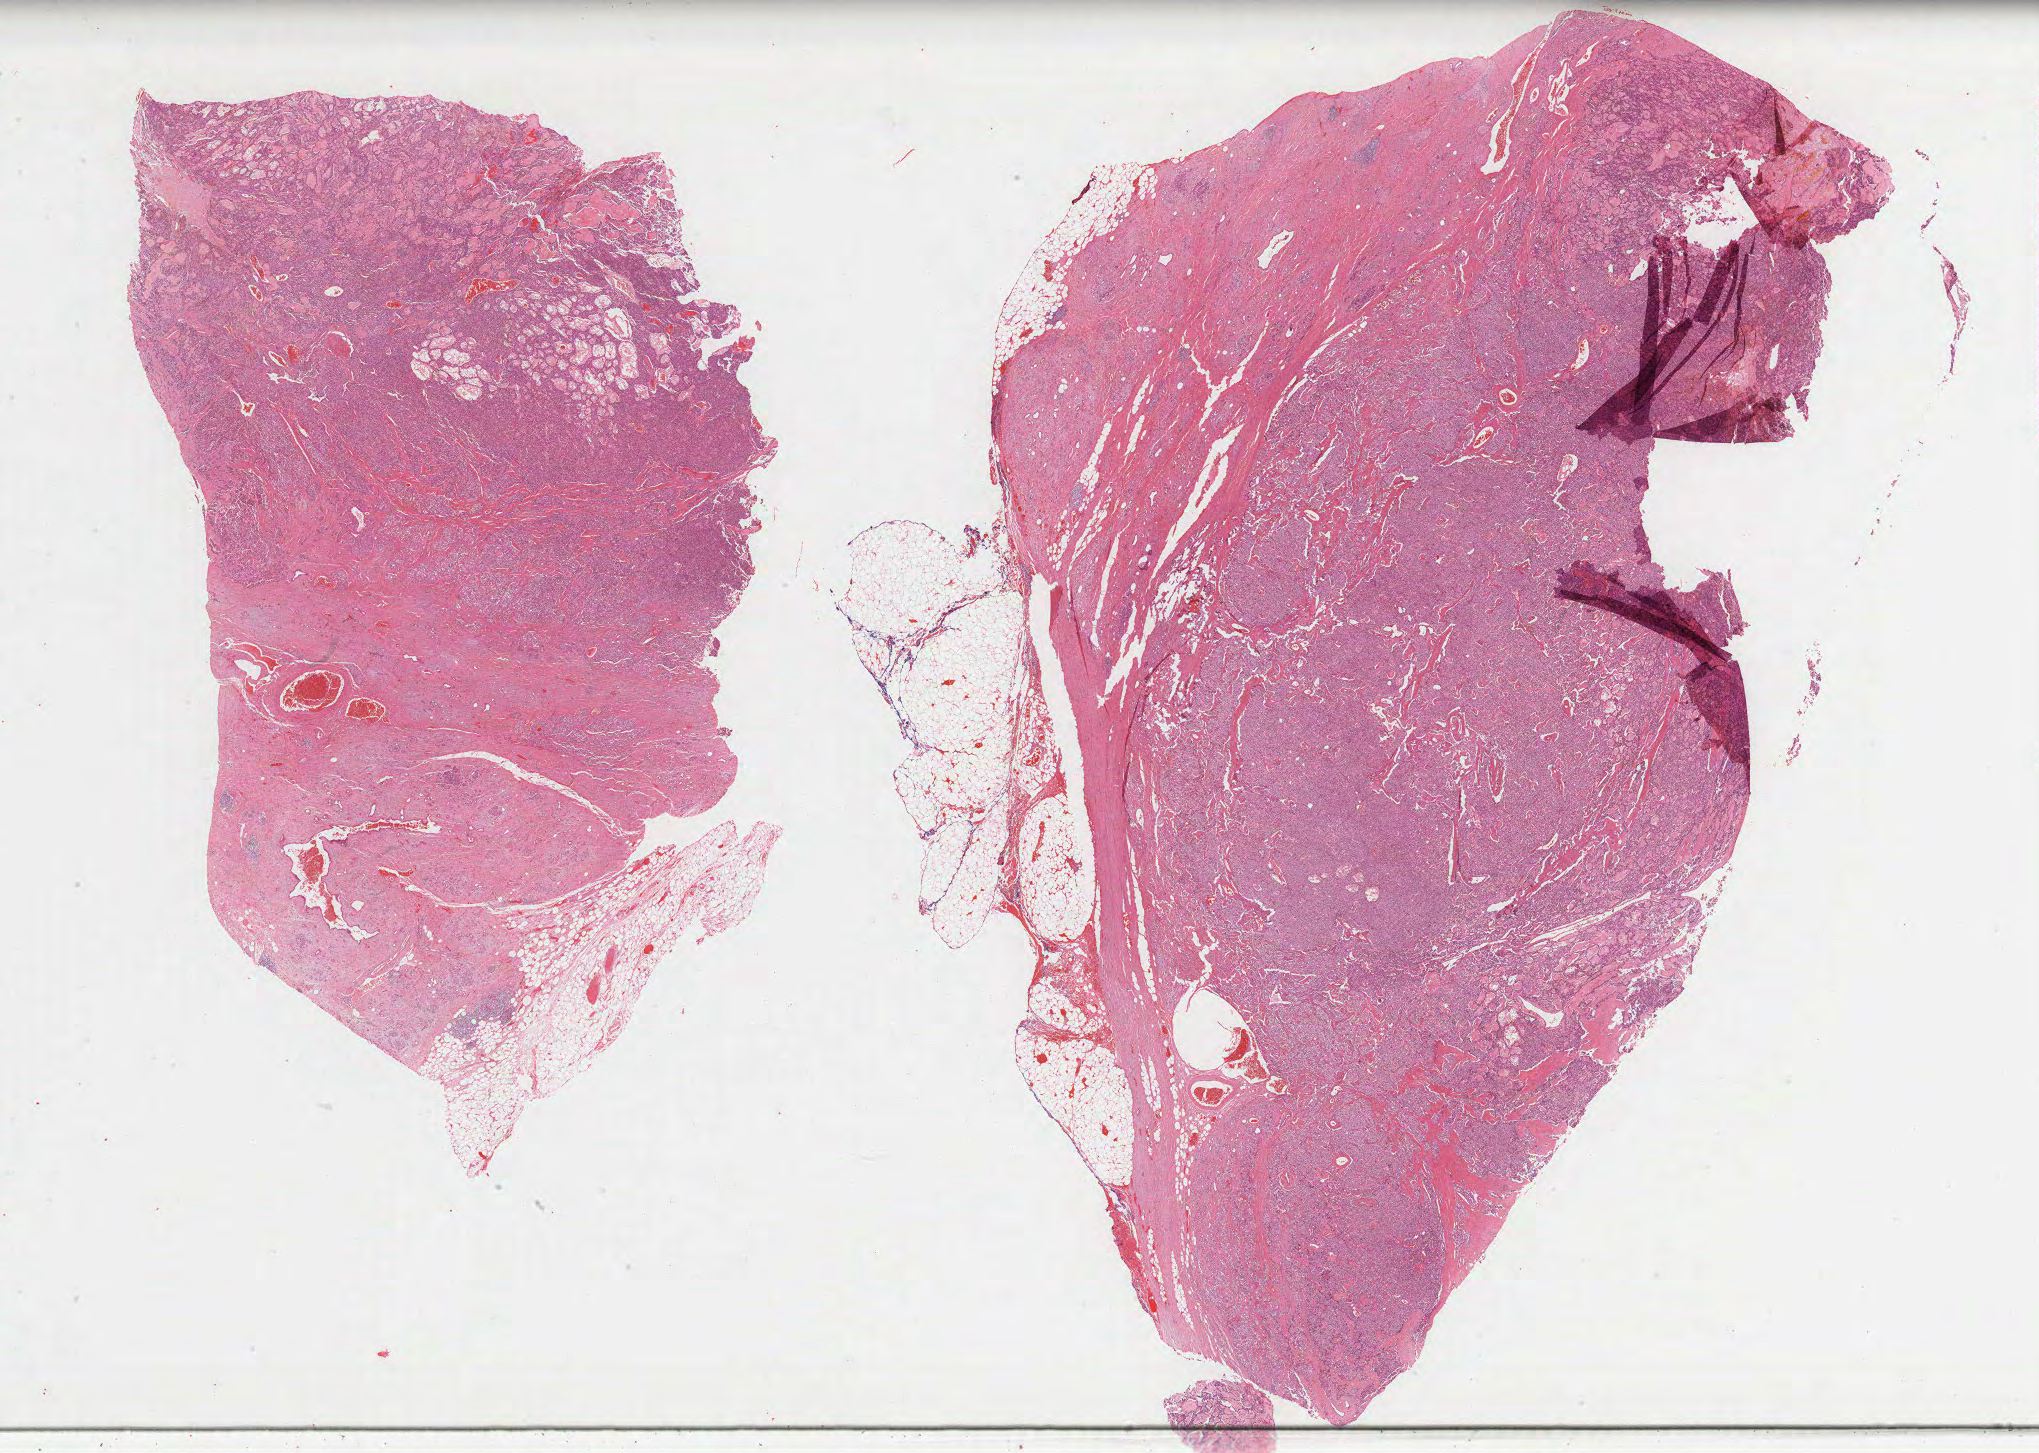
H&E whole-slide image, whole scanned area (about 32.9 x 23.5 mm) shown as a low-resolution overview; formalin-fixed paraffin-embedded (FFPE) diagnostic section; sample: primary tumour, pancreas. Male, age 67 years at initial diagnosis. Histologic grade: G1 (well differentiated).
* lymph nodes positive (case pathology): 0 of 32 examined
* pathologic diagnosis: Neuroendocrine carcinoma, NOS (body of pancreas)
* AJCC pathologic stage: IB (7th edition)